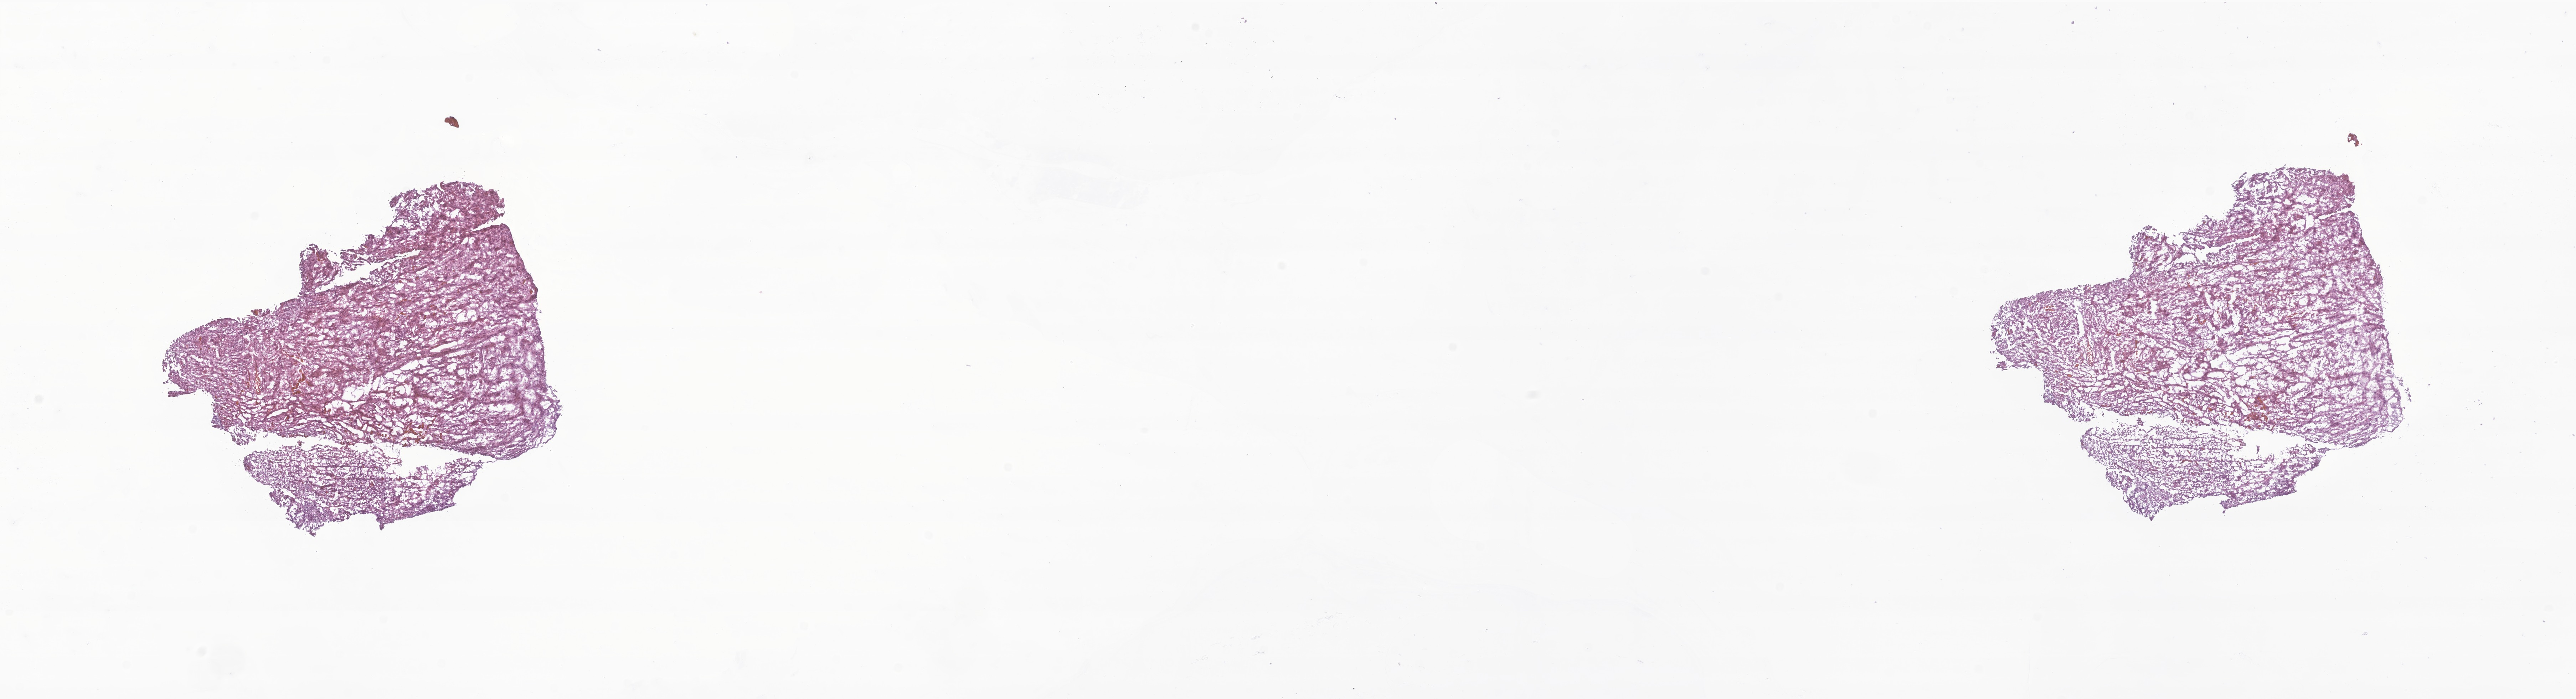
H&E whole-slide image of tumor tissue from the brain — low-resolution overview of the scanned area, about 30.5 x 8.3 mm; frozen section. Patient: female, age 327 days.
- diagnosis: Glioma, malignant